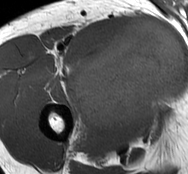
MRI of an extremity soft-tissue mass, one axial slice. Slice 52 of 93 in the series (ordered by position). MR volume resampled by the dataset authors to the PET/CT grid (not the native acquisition matrix). 3.27 mm slice thickness. 188 × 174 image matrix. Male patient. From the clinical record (not read from this slice): histological type: undifferentiated - pleiomorphic; grade: high; site of the primary tumour: right thigh.
Outlined on this slice (expert contour drawn on MRI and transferred to this co-registered scan by the dataset authors):
- gross tumour volume including surrounding oedema: bounding box (x1, y1, x2, y2) in pixels: (72, 21, 185, 129)
- gross tumour volume (mass): (75, 21, 185, 129)